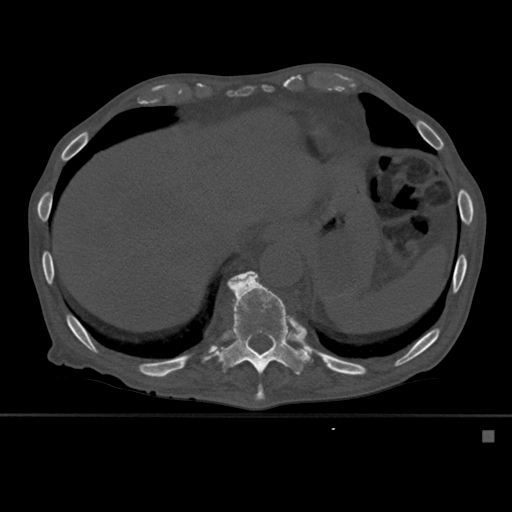
CT including the spine, one axial slice; slice 299 of 527 in the series (ordered by position); bone window (W 1800 / L 400 HU); 1.5 mm slice thickness; 512 × 512 image matrix, field of view 373 × 373 mm. Patient: male, 78 years. From the clinical record (not read from this slice): primary cancer: prostate.
Structures marked on this image (semi-automatic segmentation, software-assisted and operator-edited):
- T10 vertebra: bounding box <238,272,265,401> (left, top, right, bottom; pixels)
- T11 vertebra: <202,271,312,375>